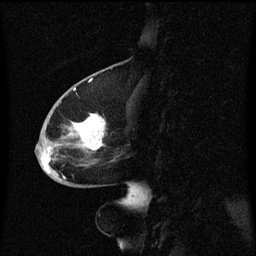
Breast MRI (dynamic contrast-enhanced), one sagittal slice. Slice 27 of 60 in the series (ordered by position). Dynamic contrast-enhanced series, image 2 of 3 at this slice position (ordered by acquisition). 1.5 T. TE 4.2 ms, TR 8.4 ms. 2 mm slice thickness. 256 × 256 image matrix. Patient: female, 68 years. Case-level facts recorded for this patient, not image findings: setting: breast cancer imaged before/during neoadjuvant chemotherapy; receptor status: triple-negative.
Annotated regions visible in this slice (semi-automatically segmented with operator editing):
- analysis volume of interest (the breast-tissue region the enhancement analysis was run in; not a lesion): bounding box <36,94,119,173> (left, top, right, bottom; pixels)
- tumour enhancement mask (voxels above the 70 % enhancement threshold inside the analysis volume of interest): <42,114,107,173>